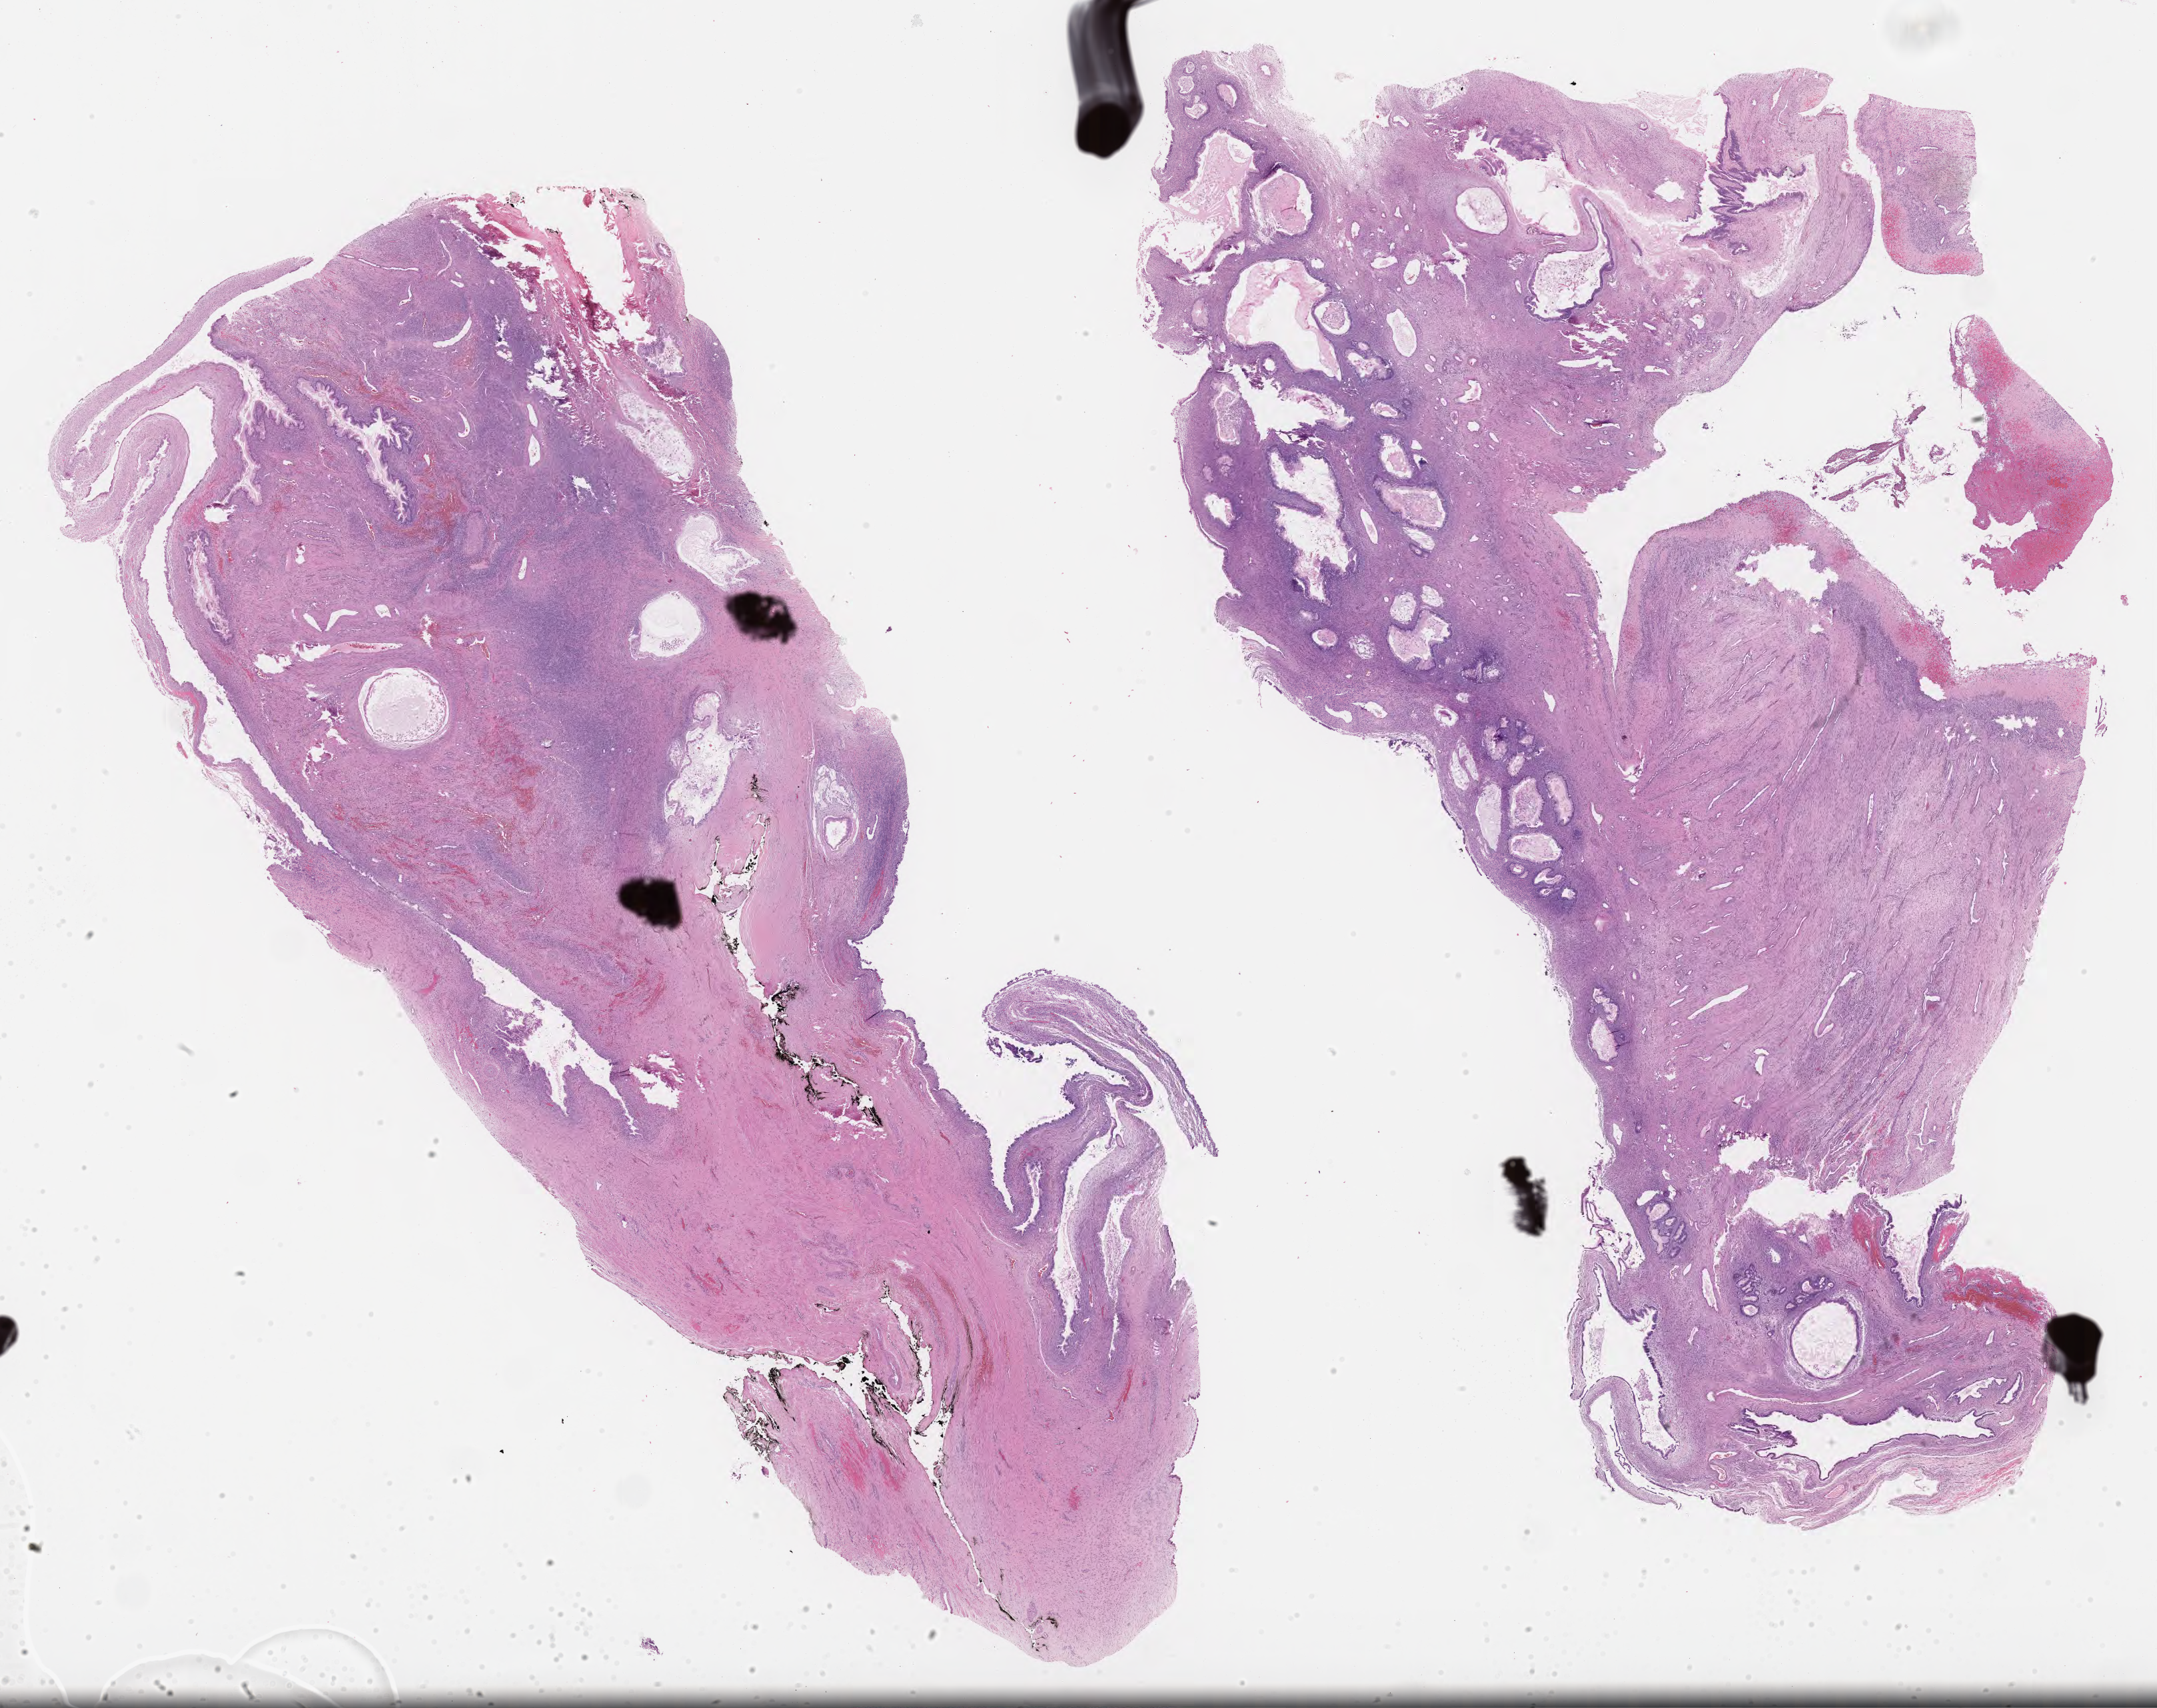
Digitized haematoxylin and eosin-stained section, shown as a low-resolution overview of the whole scanned area (about 26.1 x 20.7 mm); formalin-fixed paraffin-embedded section; primary tumor; anatomic site: ovary (right). Female patient; age at initial diagnosis 32 years. Pathologist review of this section (percent, as recorded): tumor cells 40%, tumor nuclei 45%, stromal cells 60%, necrosis 0%, normal cells 5%. Inflammatory infiltration, as recorded: lymphocyte infiltration 7%, monocyte infiltration 20%, neutrophil infiltration 0%.
Section: top of the tissue portion. Histologic diagnosis: Mucinous adenocarcinoma. AJCC pathologic stage: Stage IIIA2.